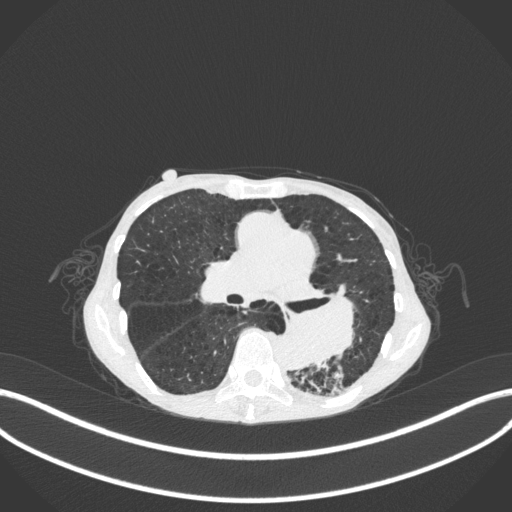
Chest CT, one axial slice; slice 154 of 347 in the series (ordered by position); reconstruction kernel B31f; 120 kVp; lung window (W 1500 / L -600 HU); 1 mm slice thickness; 512 × 512 image matrix, field of view 400 × 400 mm. Female patient, age 70 years. From the clinical record (not read from this slice): clinical TNM (as recorded): T3 N0 M0.
Outlined on this slice (bounding box drawn by a radiologist):
- lung tumour (recorded histology: small cell carcinoma): bounding box (x1, y1, x2, y2) in pixels: (280, 284, 366, 369)